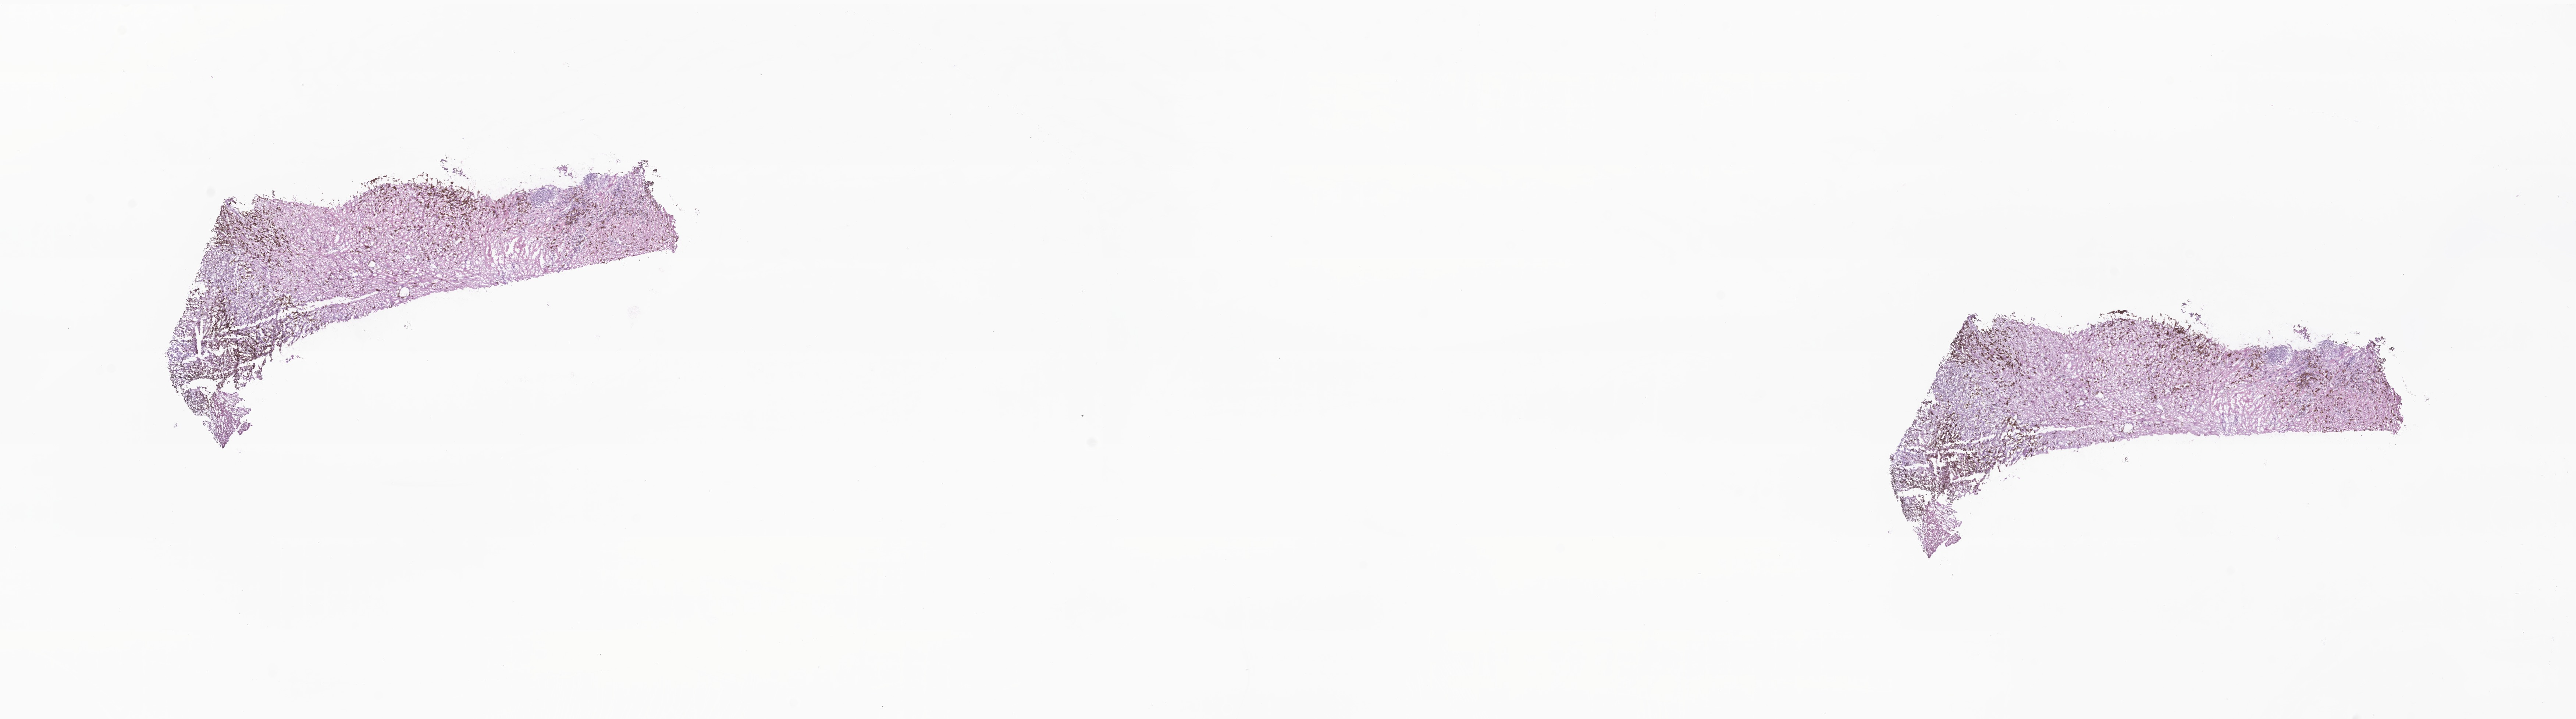
Digitized H&E-stained section, a low-resolution overview of the entire scanned area, about 29.5 x 8.2 mm, frozen section, metastatic tumor tissue, resected from lymph node. Female, age 70 years at initial diagnosis. Composition of this section per pathologist review: tumor cells 70%, tumor nuclei 80%, stromal cells 20%, necrosis 10%, normal cells 0%. Inflammatory infiltration, as recorded: lymphocyte infiltration 0%, monocyte infiltration 0%, neutrophil infiltration 0%.
Patient diagnosis (primary): Malignant melanoma, NOS. Section: top of the tissue portion.